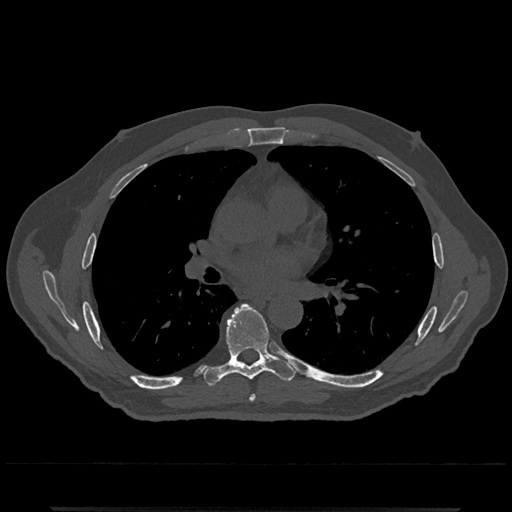
CT including the spine, one axial slice; position 727 of 797 along the scan axis; bone window (W 1800 / L 400 HU); 0.5 mm slice thickness; 512 × 512 image matrix, field of view 393 × 393 mm. Male patient, age 67 years. From the clinical record (not read from this slice): primary cancer: prostate.
Outlined on this slice (semi-automatically segmented with operator editing):
- T6 vertebra: bounding box [x1, y1, x2, y2] px = [249, 395, 256, 402]
- T7 vertebra: [205, 304, 296, 386]